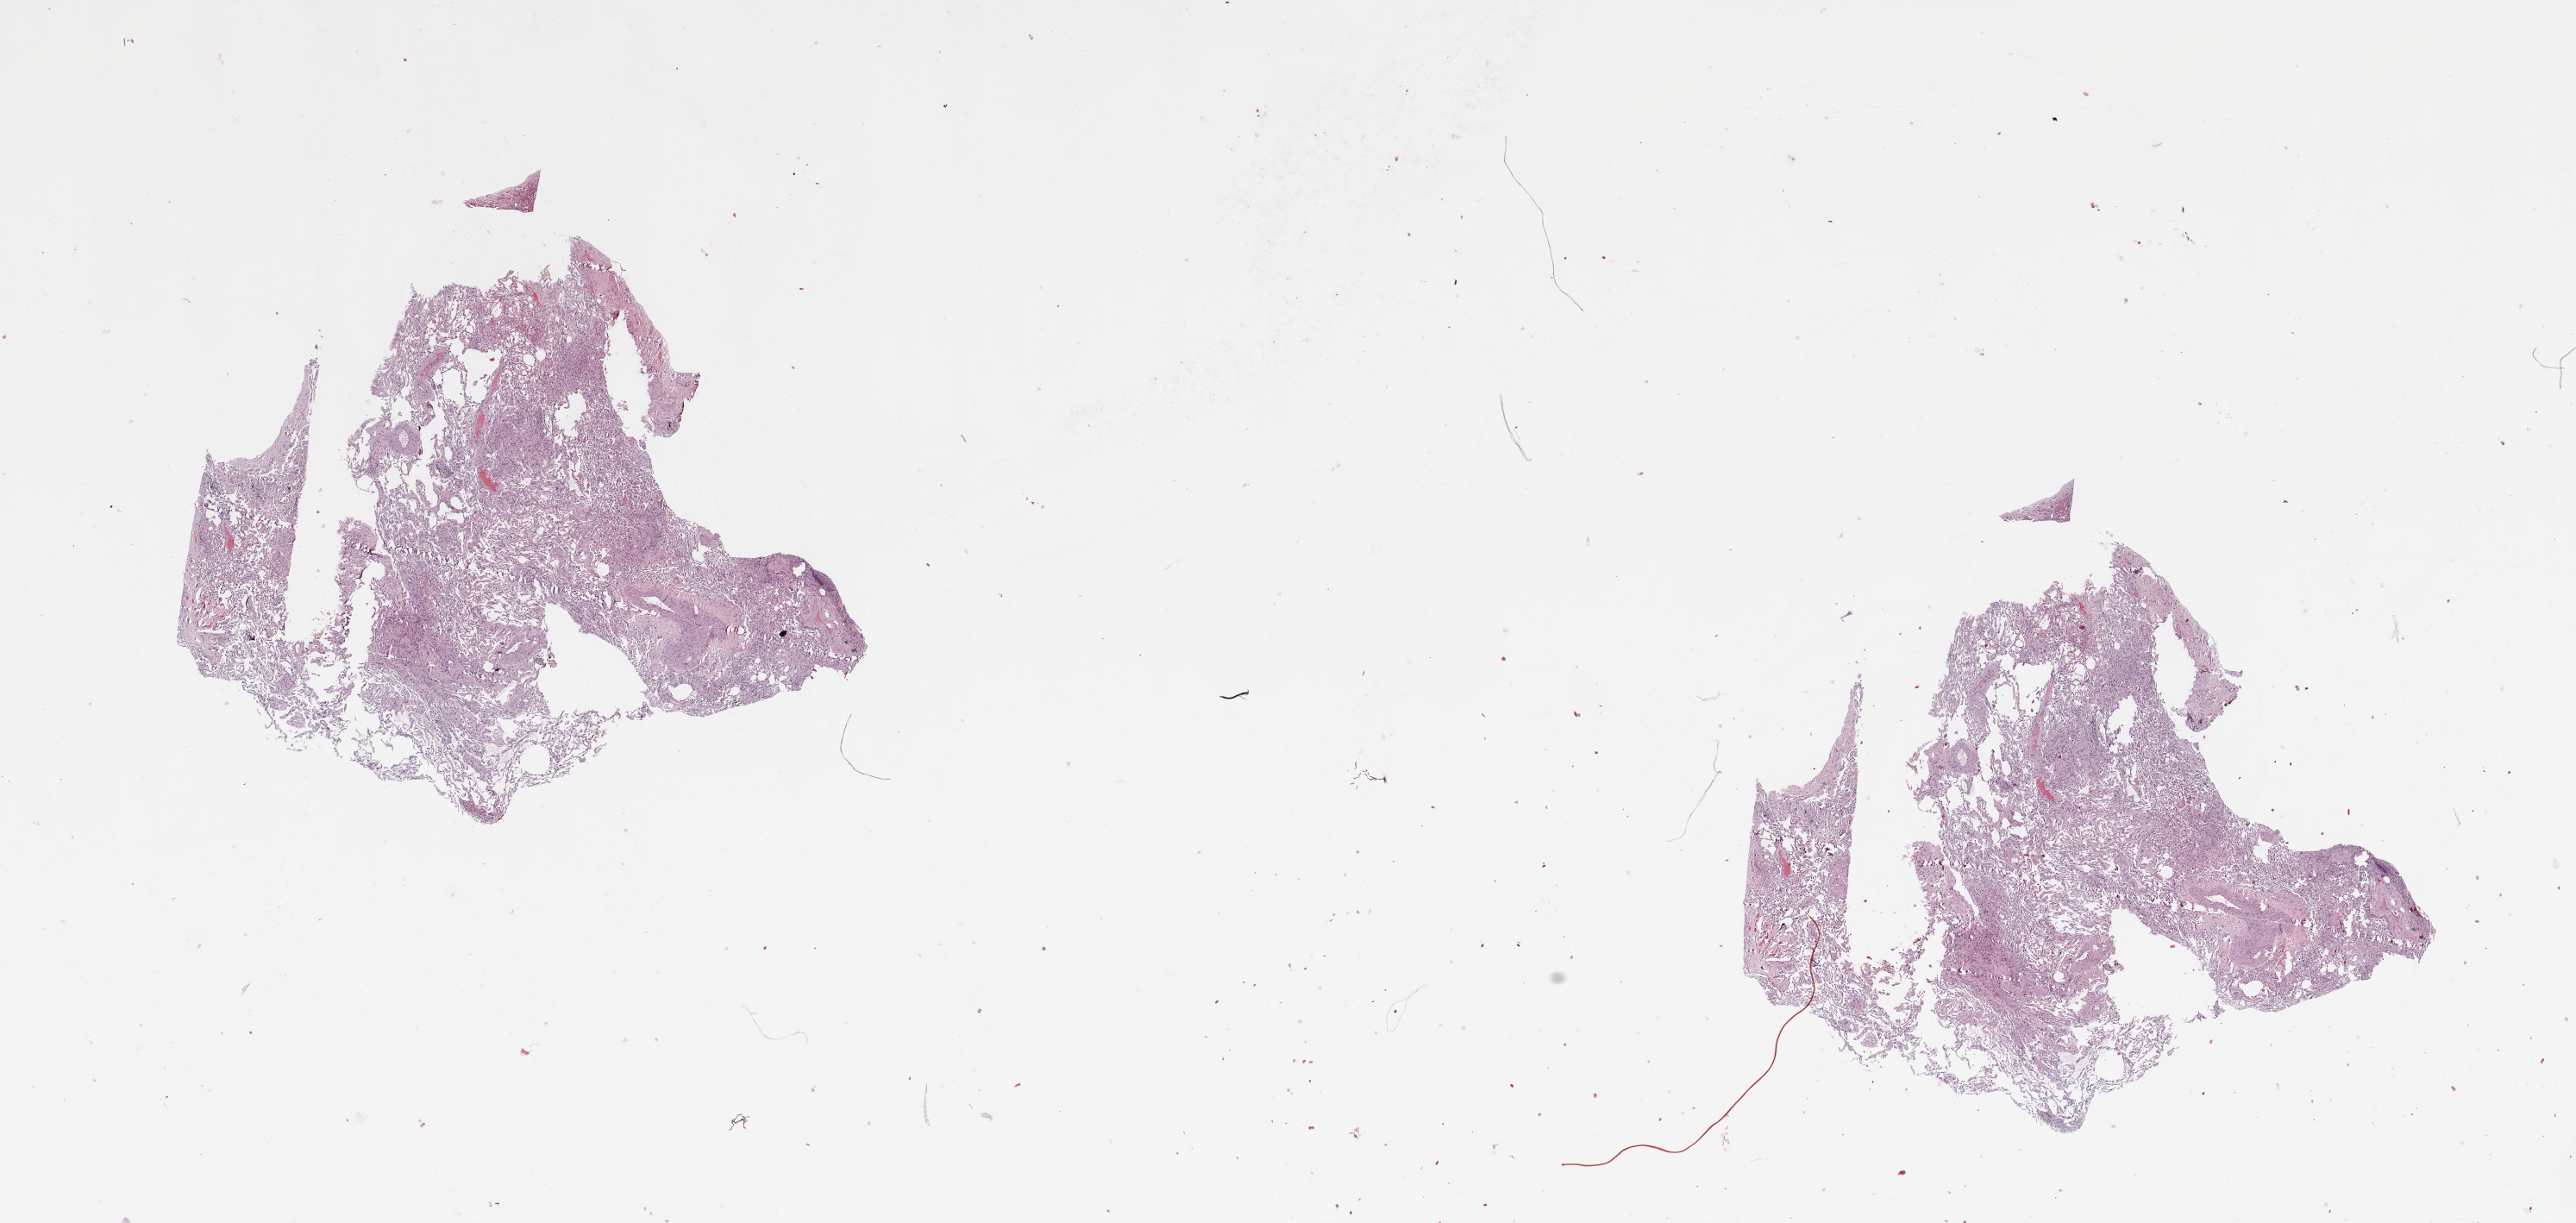
Digitized H&E-stained tissue section (whole slide) — low-resolution overview of the scanned area, about 23.6 x 11.2 mm, lung, normal (non-tumour) tissue. 66-year-old male patient.
This section: normal (non-tumour) tissue from the same patient. Patient diagnosis: Squamous cell carcinoma, NOS.